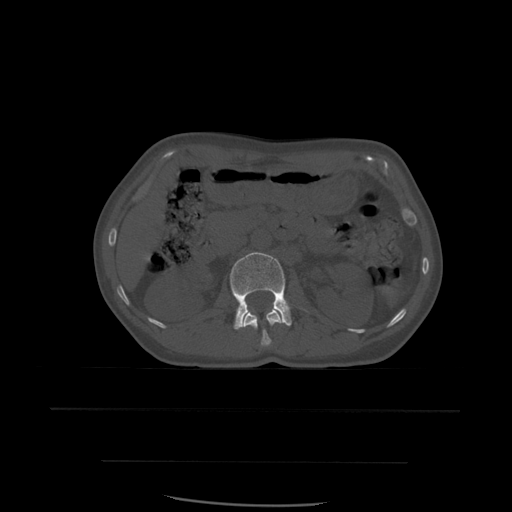
CT including the spine, one axial slice; slice 234 of 574 in the series (ordered by position); bone window (W 1800 / L 400 HU); 1.25 mm slice thickness; 512 × 512 image matrix. Patient age 48 years. From the clinical record (not read from this slice): primary cancer: lung; vertebrae with lytic lesions (as recorded): T11.
Outlined on this slice (semi-automatically segmented with operator editing):
- L1 vertebra: bounding box (x1, y1, x2, y2) in pixels: (242, 310, 284, 347)
- L2 vertebra: (230, 252, 292, 330)